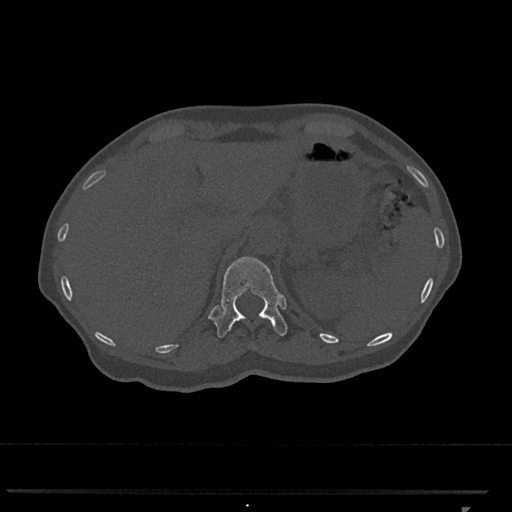
CT including the spine, one axial slice. Position 472 of 793 along the scan axis. 120 kVp. Bone window (W 1800 / L 400 HU). 0.5 mm slice thickness. 512 × 512 image matrix. Patient: female, 62 years. Case-level facts recorded for this patient, not image findings: primary cancer: renal.
Outlined on this slice (semi-automatically segmented with operator editing):
- T12 vertebra: bounding box [x1, y1, x2, y2] px = [215, 256, 287, 338]